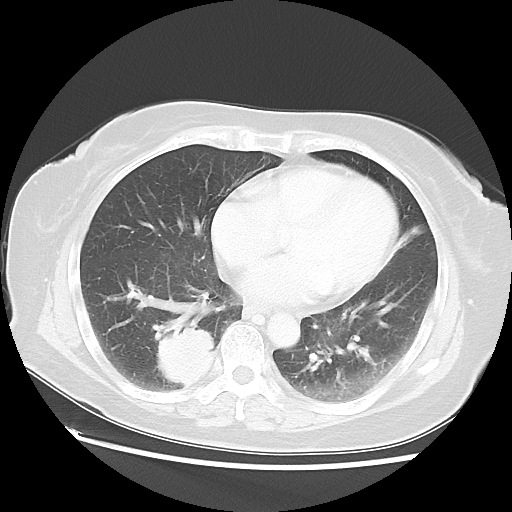
Chest CT, one axial slice; slice 23 of 52 in the series (ordered by position); reconstruction kernel LUNG; 120 kVp; lung window (W 1500 / L -600 HU); 5 mm slice thickness; 512 × 512 image matrix. Female patient, age 69 years. Case-level facts recorded for this patient, not image findings: clinical TNM (as recorded): T2 N1 M1a.
Outlined on this slice (bounding box drawn by a radiologist):
- lung tumour (recorded histology: adenocarcinoma): box from (x=151, y=318) to (x=216, y=392) px